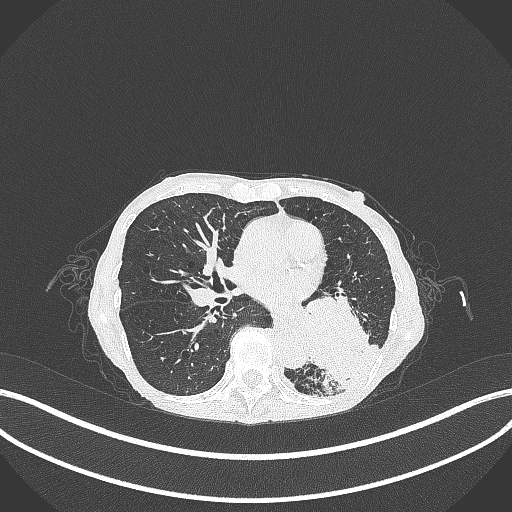
Chest CT, one axial slice; slice 130 of 347 in the series (ordered by position); 120 kVp; lung window (W 1500 / L -600 HU); 1 mm slice thickness; 512 × 512 image matrix, field of view 400 × 400 mm. Patient: female, 70 years. Case-level facts recorded for this patient, not image findings: clinical TNM (as recorded): T3 N0 M0; histopathological grade: G3.
Outlined on this slice (rectangle marked by the reading radiologist):
- lung tumour (recorded histology: small cell carcinoma): bounding box [x1, y1, x2, y2] px = [295, 279, 377, 393]